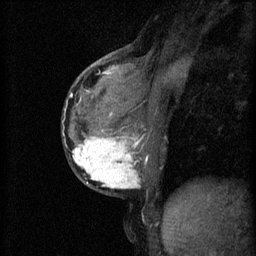
Breast MRI (dynamic contrast-enhanced), one sagittal slice; position 27 of 60 along the scan axis; 3 images stored at this slice position (order not interpretable as contrast timing); 1.5 T; TE 4.2 ms, TR 11 ms; 256 × 256 image matrix. Female patient, age 37 years.
Structures marked on this image (semi-automatically segmented with operator editing):
- analysis volume of interest (the breast-tissue region the enhancement analysis was run in; not a lesion): bounding box (x1, y1, x2, y2) in pixels: (69, 118, 157, 195)
- tumour enhancement mask (voxels above the 70 % enhancement threshold inside the analysis volume of interest): (73, 130, 147, 189)